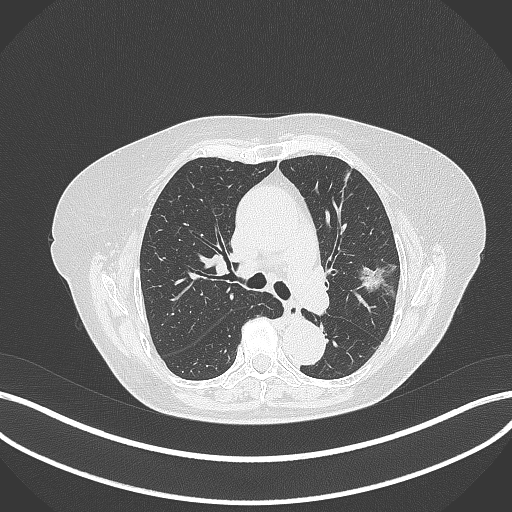
Chest CT, one axial slice. Slice 208 of 316 in the series (ordered by position). Reconstruction kernel B70f. 120 kVp. Lung window (W 1500 / L -600 HU). 1 mm slice thickness. 512 × 512 image matrix. Patient: female, 75 years. From the clinical record (not read from this slice): clinical TNM (as recorded): T1c N0 M0.
Annotated regions visible in this slice (rectangle marked by the reading radiologist):
- lung tumour (recorded histology: adenocarcinoma): bounding box [x1, y1, x2, y2] px = [353, 263, 386, 297]